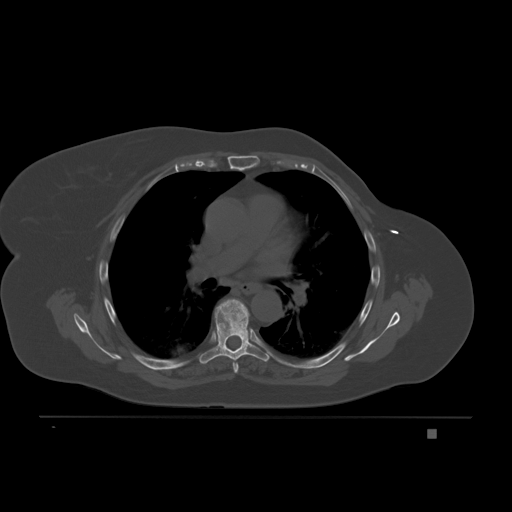
CT including the spine, one axial slice. Slice 138 of 221 in the series (ordered by position). Bone window (W 1800 / L 400 HU). 3 mm slice thickness. 512 × 512 image matrix. Female patient, age 63 years. Case-level facts recorded for this patient, not image findings: primary cancer: breast.
Outlined on this slice (semi-automatic segmentation, software-assisted and operator-edited):
- T5 vertebra: bounding box (x1, y1, x2, y2) in pixels: (233, 360, 239, 373)
- T6 vertebra: (199, 299, 270, 364)